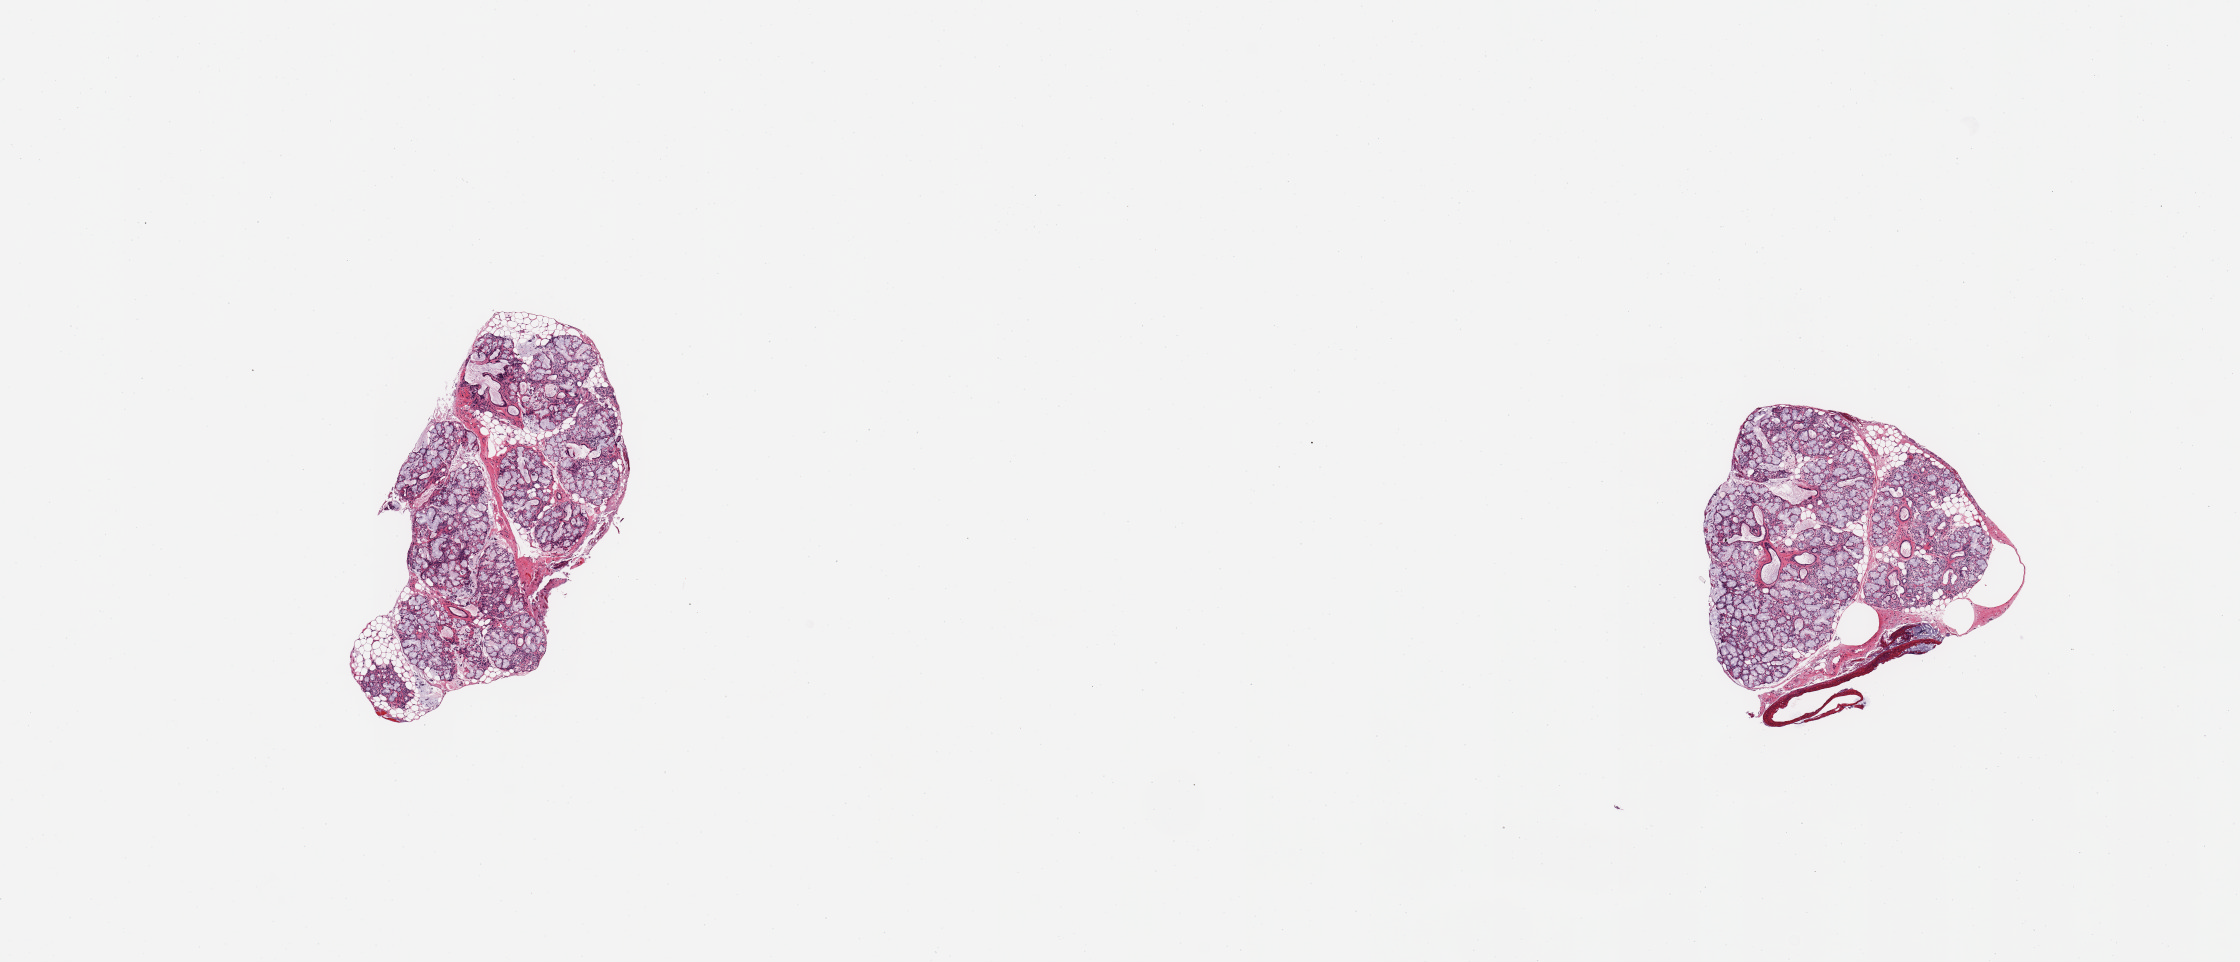
Haematoxylin and eosin whole-slide image — whole scanned area (about 17.7 x 7.6 mm) shown as a low-resolution overview; PAXgene-fixed, paraffin-embedded tissue; section of minor salivary gland (target tissue); tissue donor sample. Male donor.
• pathologist's review note for this sample: 2 pieces, ~98% glandular parenchyma; trace rim of fat